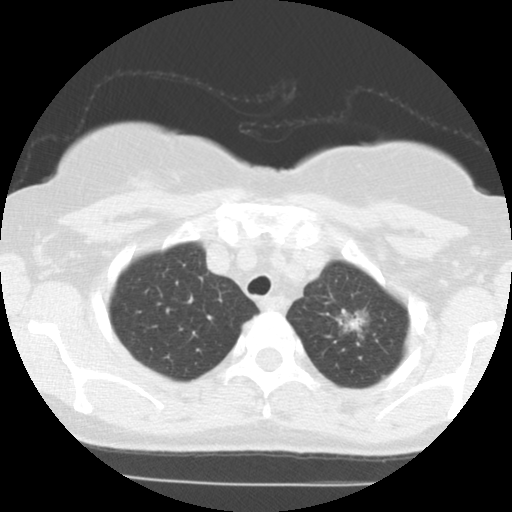
Low-dose screening chest CT, one axial slice; slice 101 of 123 in the series (ordered by position); reconstruction kernel STANDARD; lung window (W 1500 / L -600 HU); 512 × 512 image matrix.
Annotated regions visible in this slice (expert manual segmentation):
- lesion 1 (tumor, upper lobe of left lung): bounding box <335,309,368,338> (left, top, right, bottom; pixels)